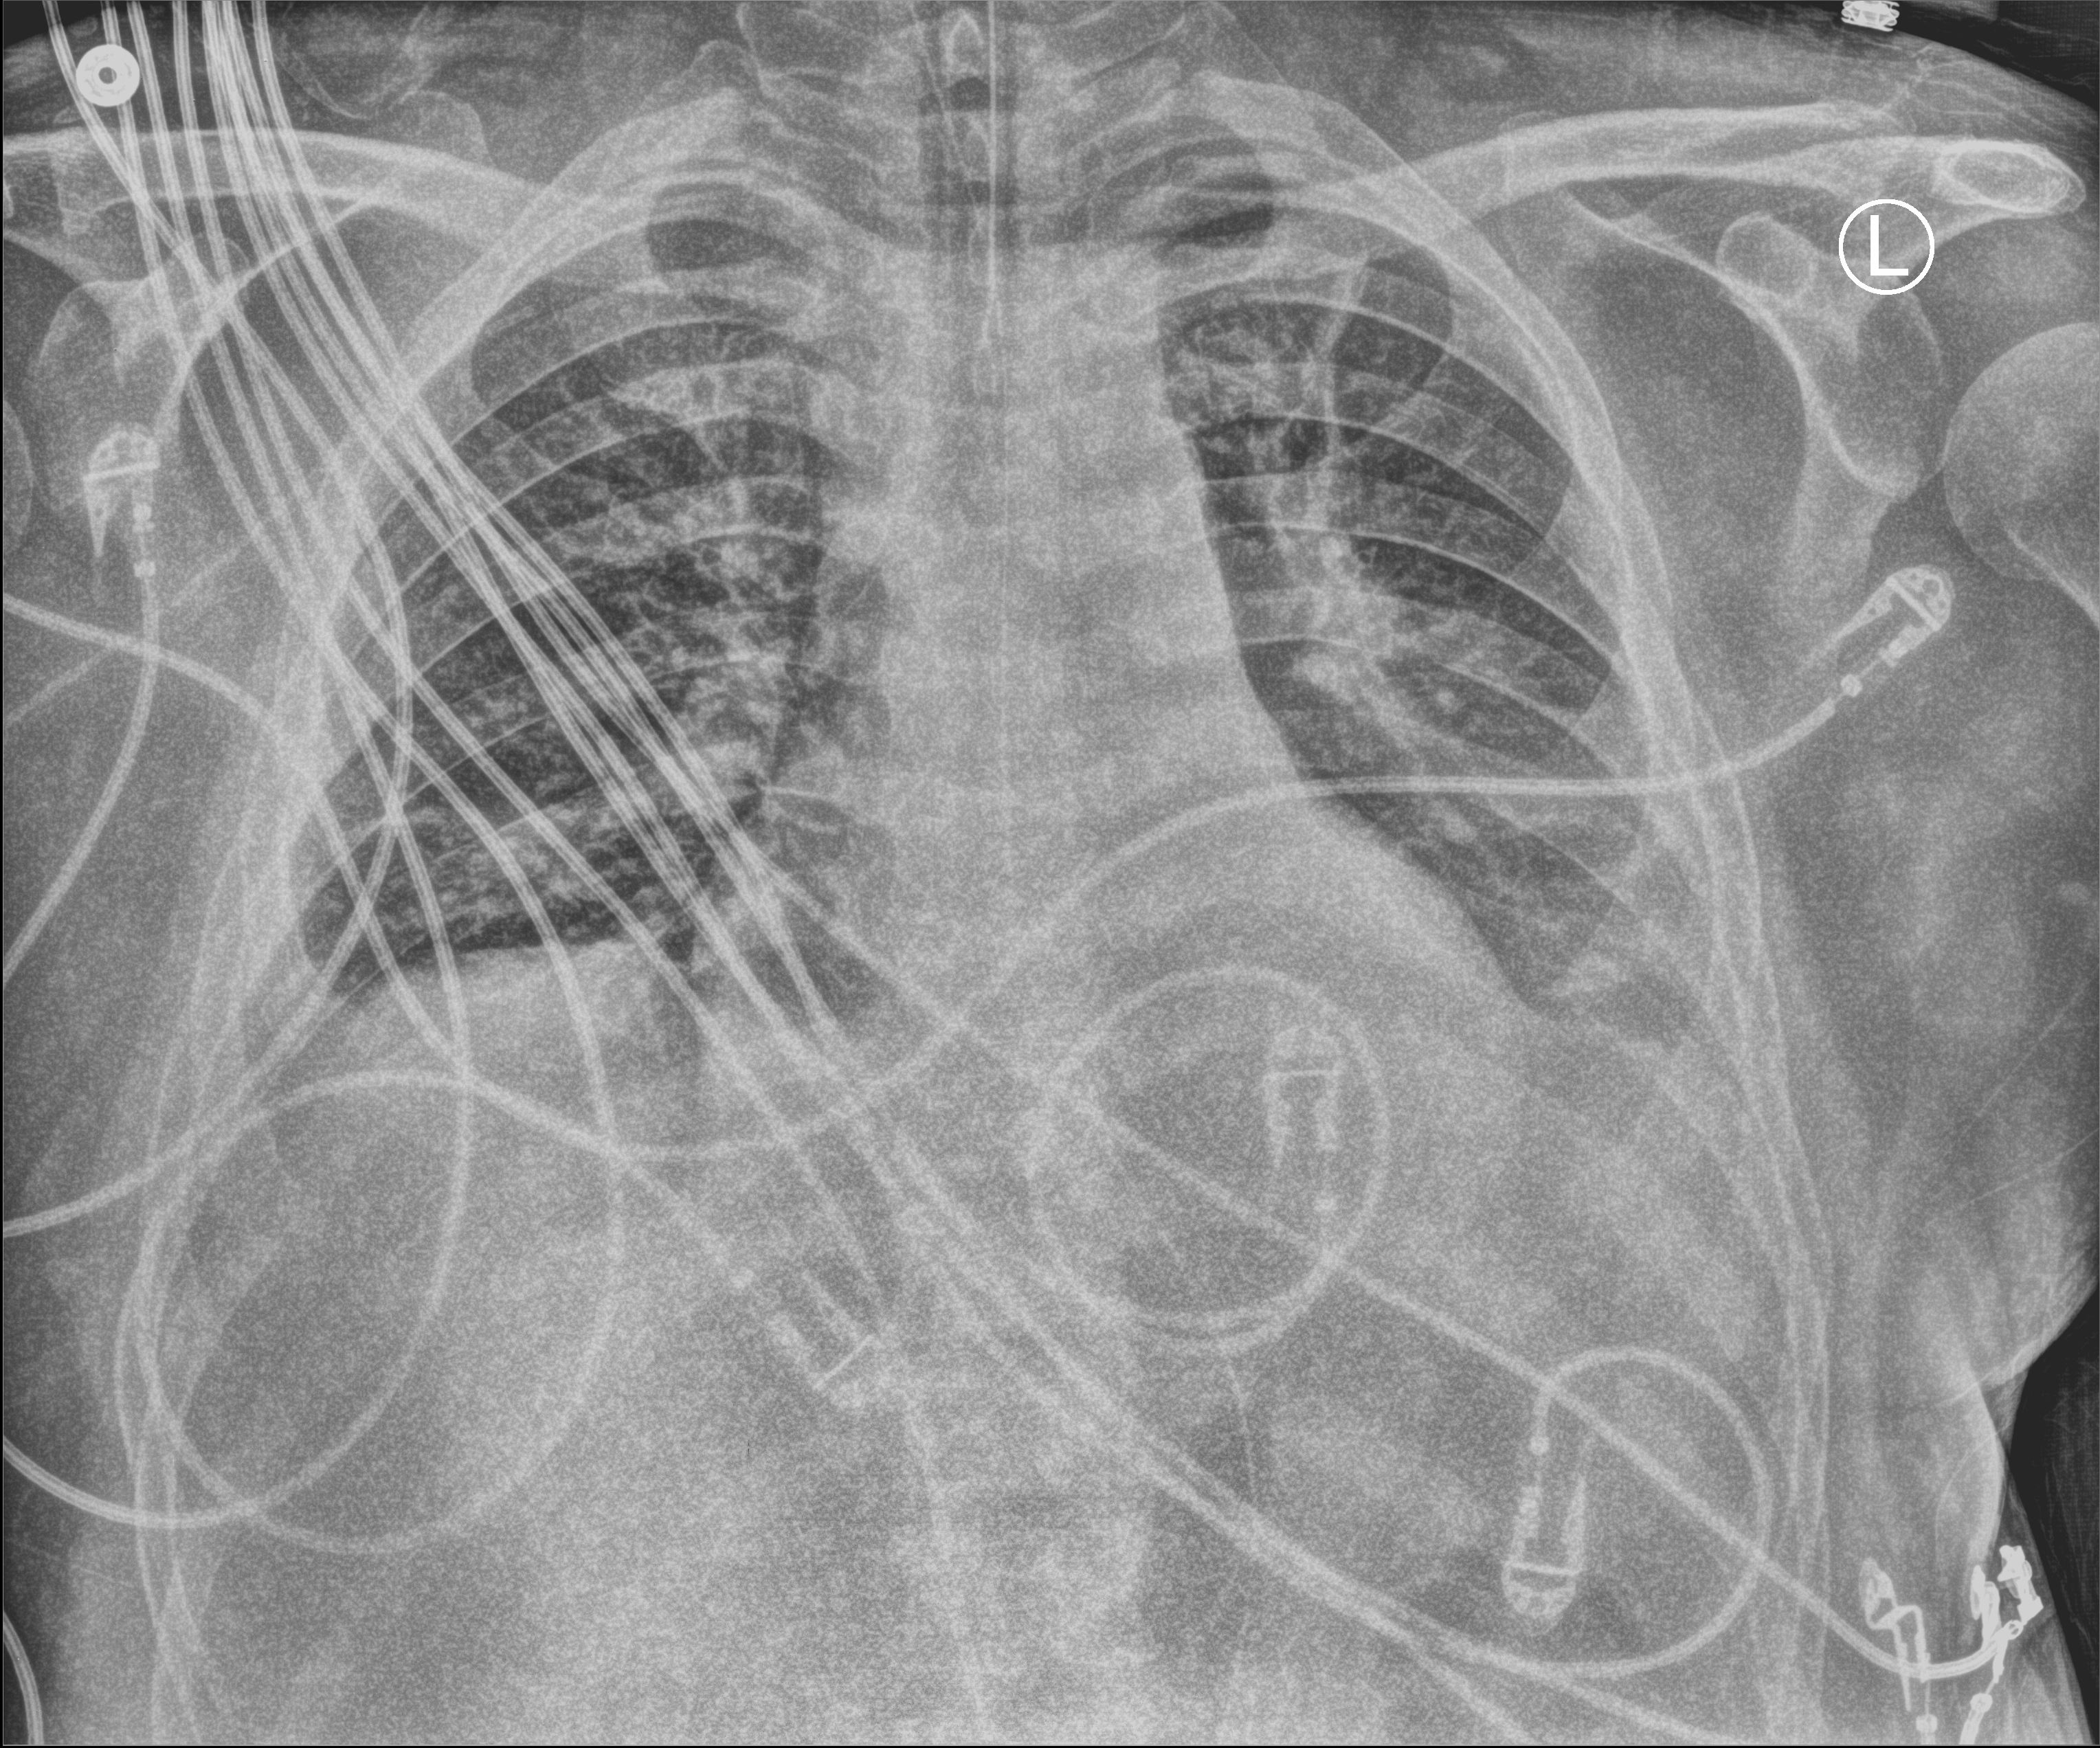
Portable chest radiograph; anteroposterior (AP) projection. Patient hospitalised with COVID-19; male, aged 18–59 years.
Admission-level facts for this patient (not findings on this image; timing relative to this image not recorded):
- mechanically ventilated during this hospital stay: yes
- length of hospital stay: 65 days
- admitted to intensive care during this hospital stay: yes